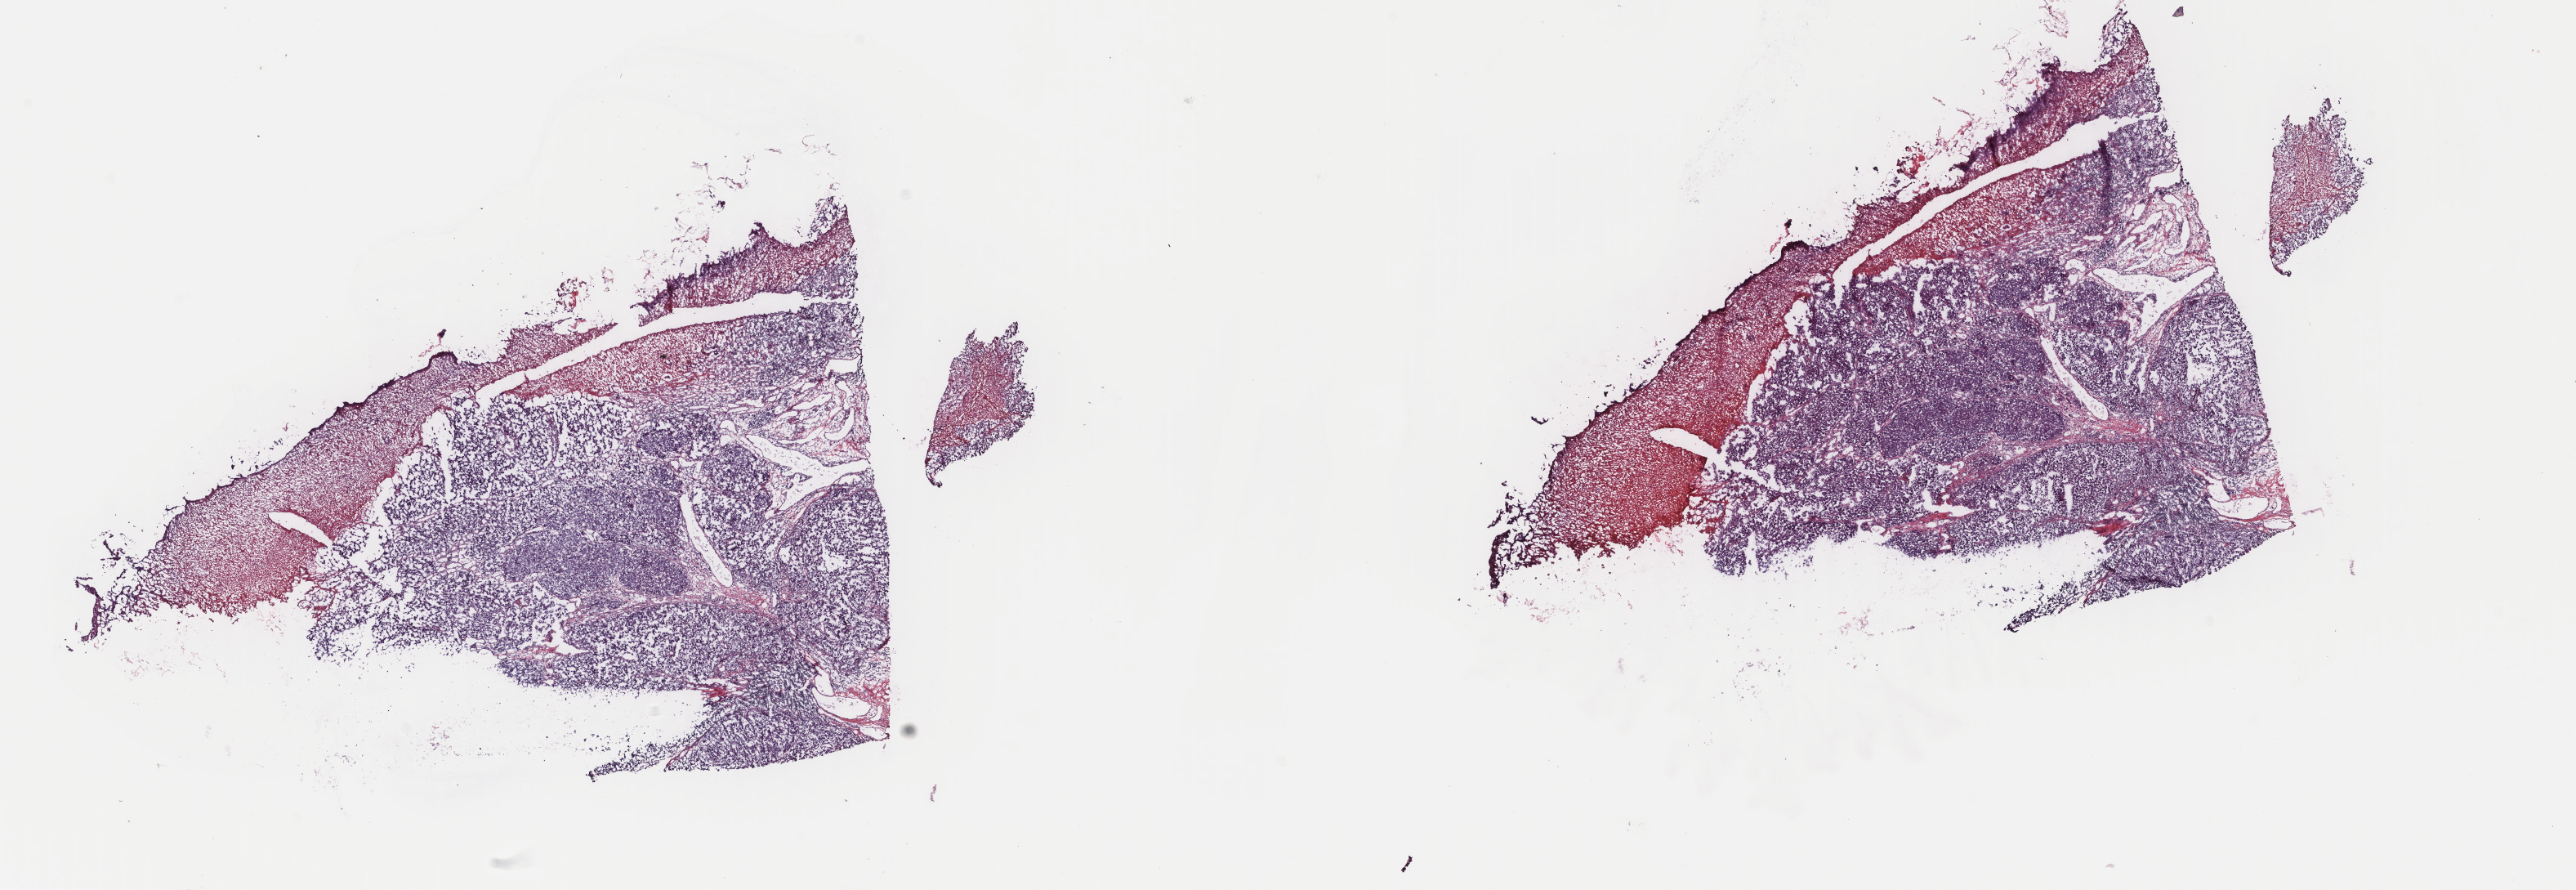
Whole-slide histology image, H&E-stained, whole scanned area (about 25.0 x 8.6 mm, acquisition: 40x scan) shown as a low-resolution overview, frozen section from the top of the tissue portion, sample: primary tumour, skin. Patient: male, age at initial diagnosis 83 years. Pathologist review of this section (percent, as recorded): tumour cells 75%, tumour nuclei 75%.
Pathologic diagnosis: Nodular melanoma.